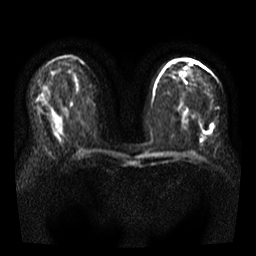
Breast MRI, one axial slice; slice 20 of 35 in the series (ordered by position); diffusion-weighted series; image 2 of 4 stored at this slice position (different b-values; order by instance number); 3 T; 5 mm slice thickness; 256 × 256 image matrix. Female patient.
Outlined on this slice (manually delineated by an expert):
- tumour on diffusion-weighted imaging: bounding box (x1, y1, x2, y2) in pixels: (202, 132, 209, 141)